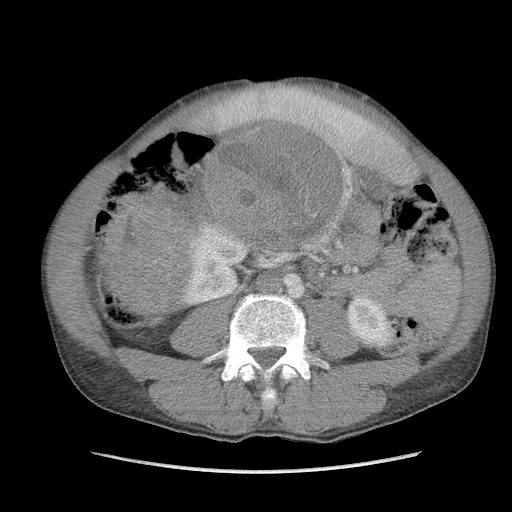
Contrast-enhanced abdominal CT, one axial slice. Slice 44 of 115 in the series (ordered by position). Soft-tissue window (W 400 / L 40 HU). 512 × 512 image matrix, field of view 360 × 360 mm. Male patient. From the clinical record (not read from this slice): diagnosis: adrenocortical carcinoma; tumour side: right adrenal; Ki-67 index: 13 %; stage (as recorded): 3.
Annotated regions visible in this slice (semi-automatic segmentation, software-assisted and operator-edited):
- mass: bounding box <105,122,345,312> (left, top, right, bottom; pixels)